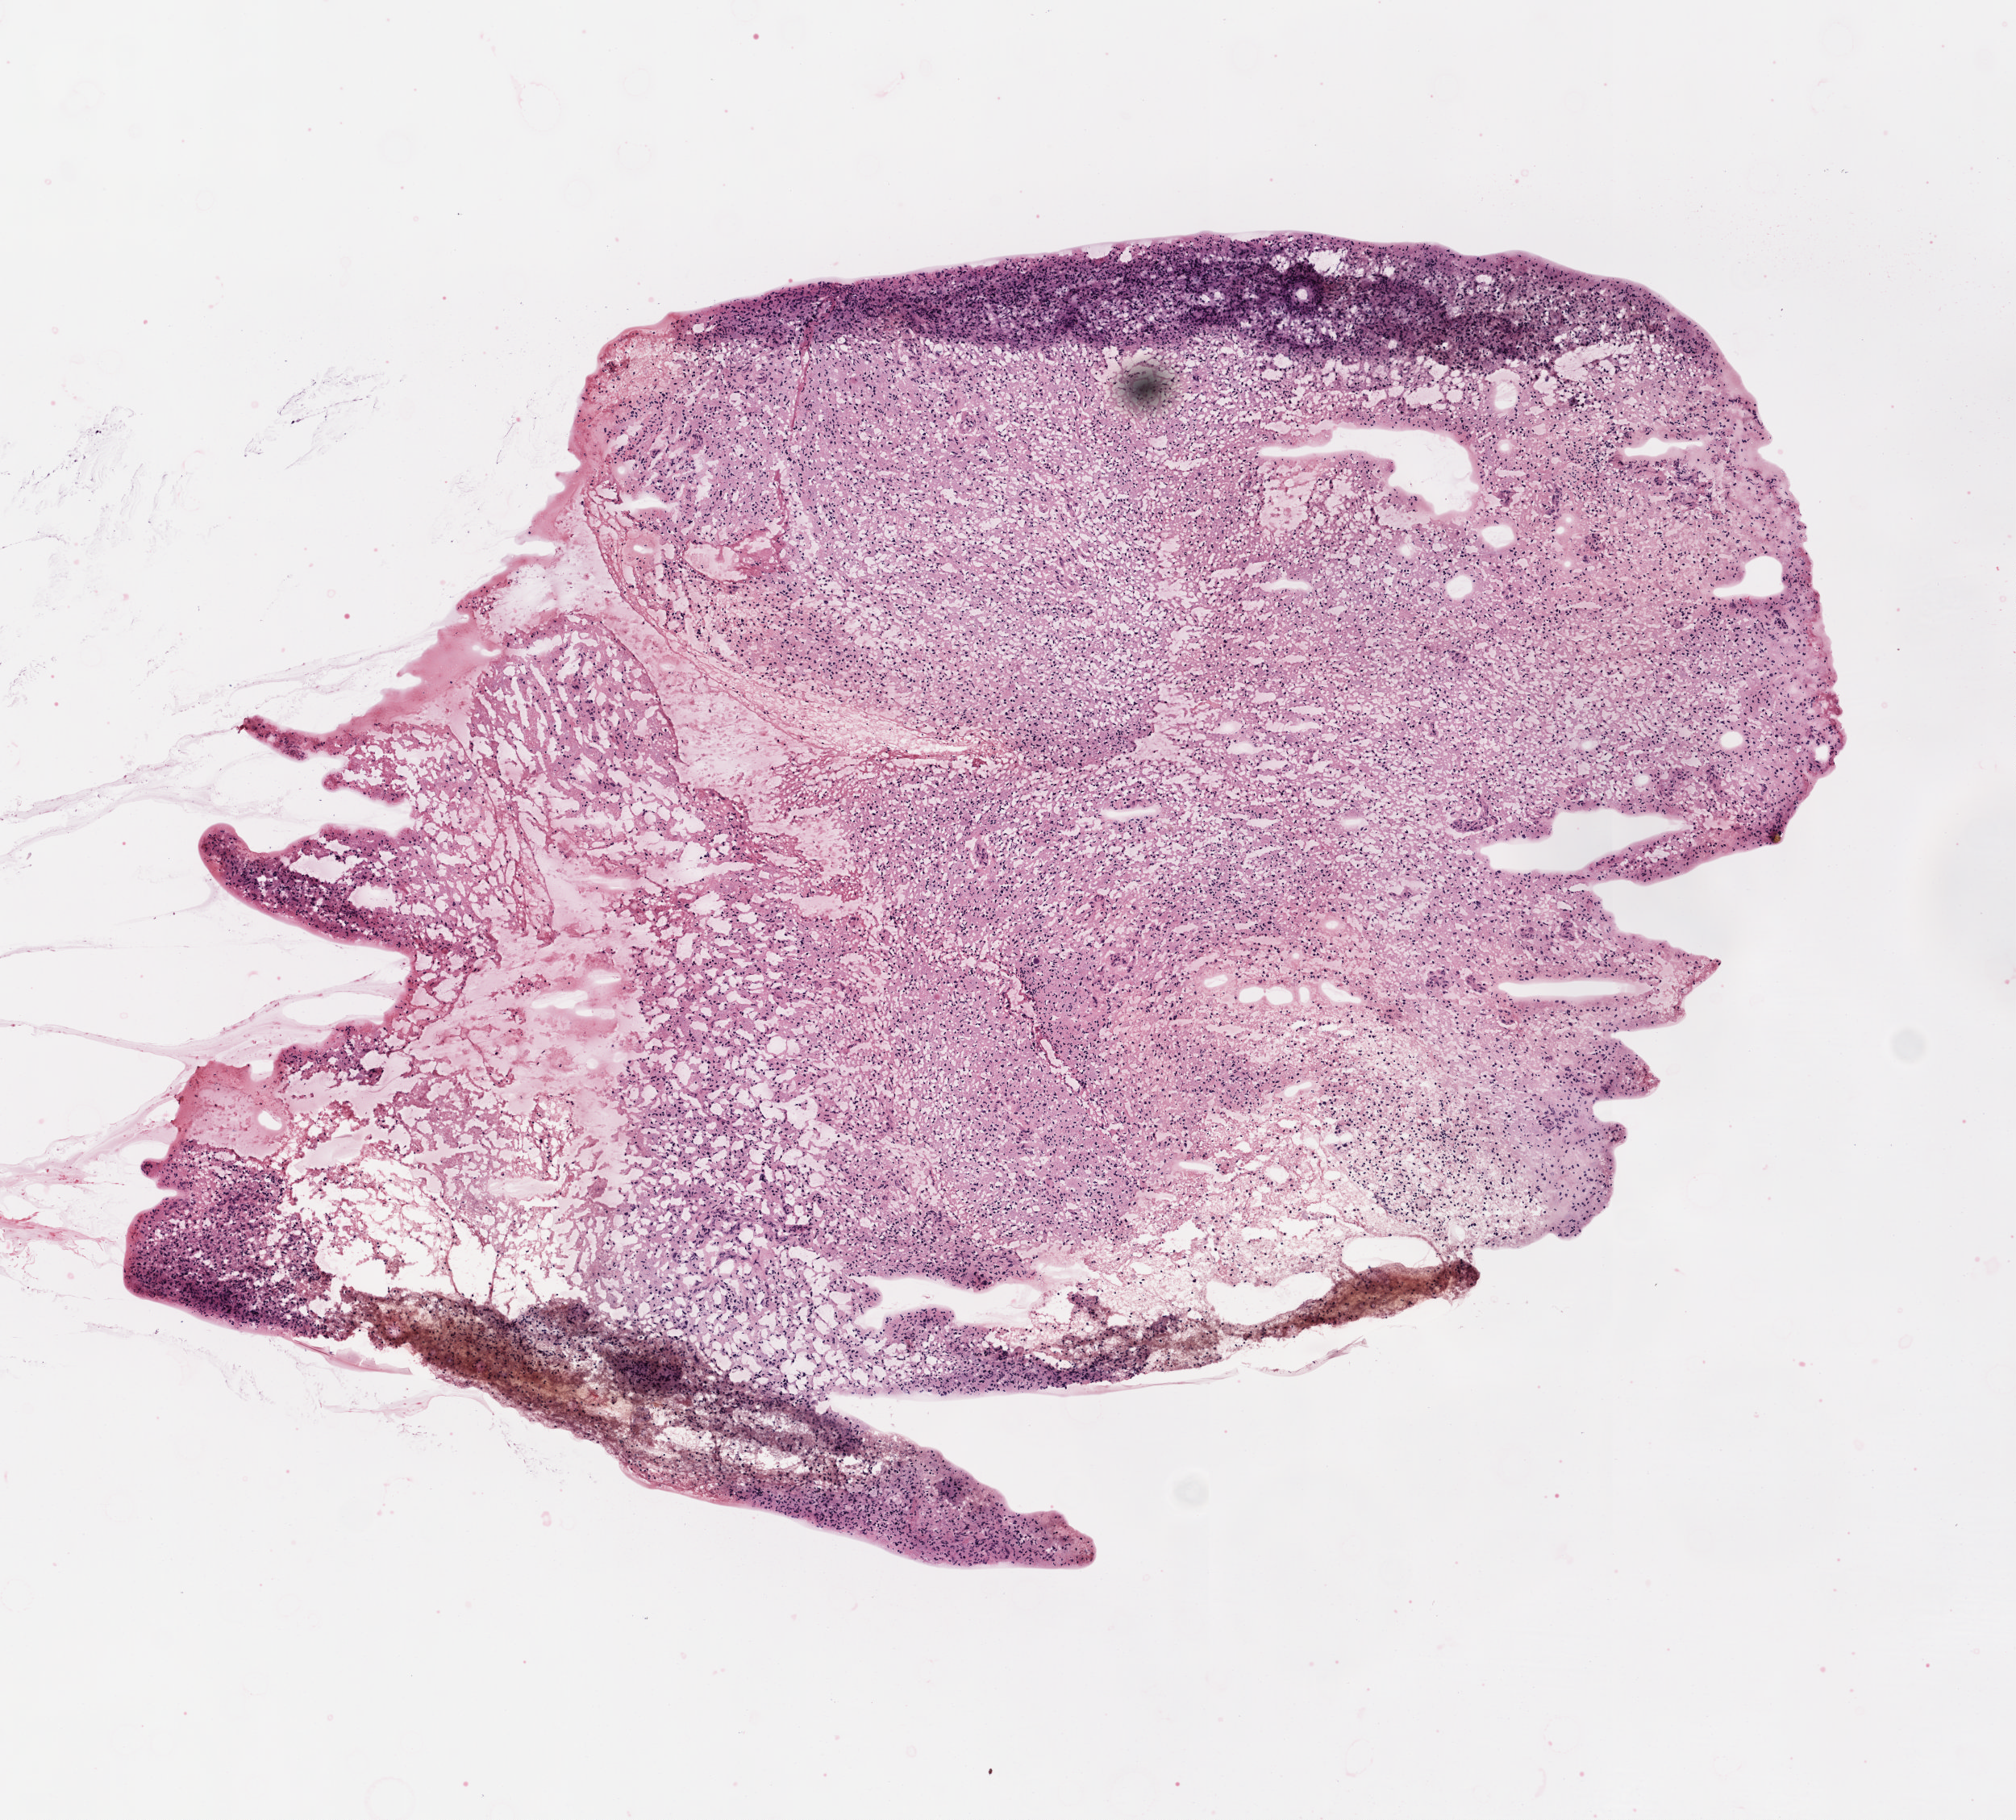
H&E whole-slide image, shown as a low-resolution overview of the whole scanned area (about 5.0 x 4.5 mm, from a 20x scan); frozen section from the top of the tissue portion; sample: primary tumour, brain. Patient: female, age at initial diagnosis 72 years. Pathologist review of this section (percent, as recorded): tumour nuclei 75%, normal cells 0%, stromal cells 0%, necrosis 0%.
* diagnosis: Glioblastoma